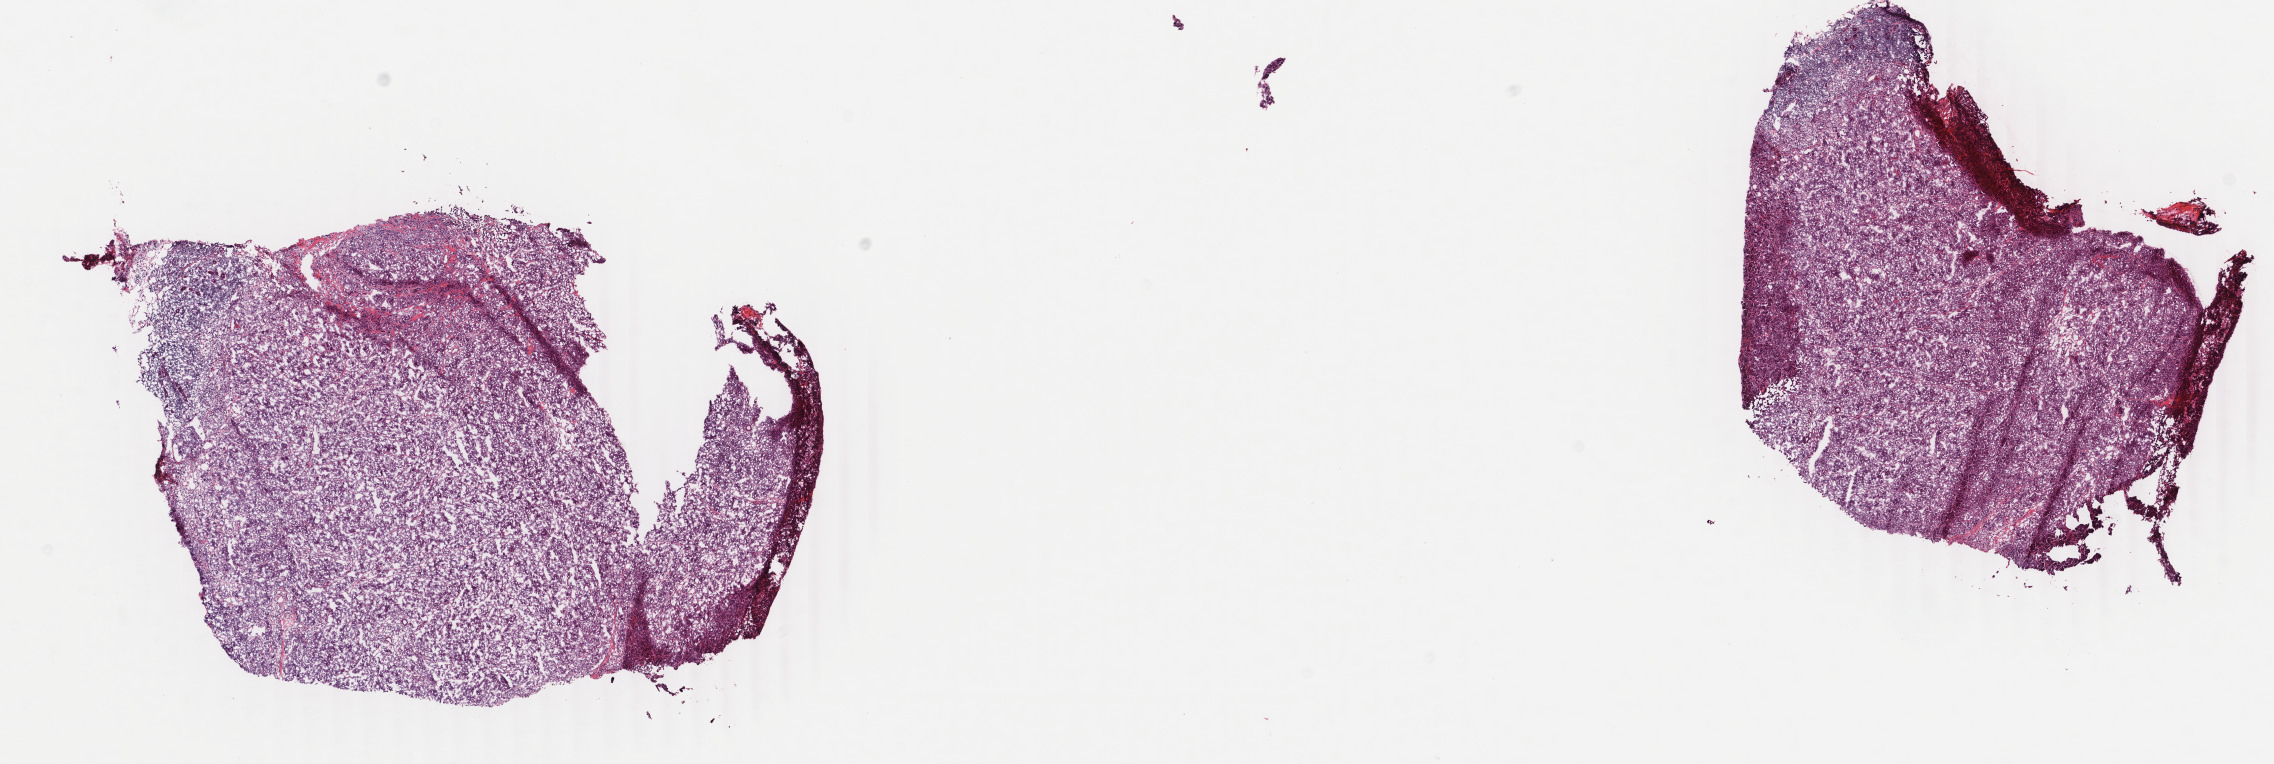
Whole-slide histology image, Hematoxylin and eosin (H&E) stained — whole scanned area (about 18.1 x 6.1 mm, slide scanned at 40x) shown as a low-resolution overview. Frozen section from the top of the tissue portion. Breast, primary tumour sample. Female, age 48 years at initial diagnosis. Slide review estimates, as recorded: tumour cells 90%, tumour nuclei 80%, normal cells 5%, stromal cells 5%, necrosis 0%. Inflammatory infiltration, as recorded: lymphocyte infiltration 10%, monocyte infiltration 0%, neutrophil infiltration 0%.
Lymph nodes positive (case pathology): 16 of 21 examined. Pathologic diagnosis: Infiltrating duct carcinoma, NOS.